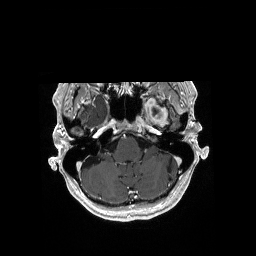
Brain MRI from a brain-tumour surgery series, one axial slice. Position 138 of 176 along the scan axis. T1-weighted post-contrast. 1 mm slice thickness. 256 × 256 image matrix, field of view 256 × 256 mm. Case-level facts recorded for this patient, not image findings: histopathology: Glioblastoma; WHO grade: 4; IDH mutation: no.
Structures marked on this image (expert manual segmentation):
- previous resection cavity: bounding box [x1, y1, x2, y2] px = [152, 109, 158, 114]